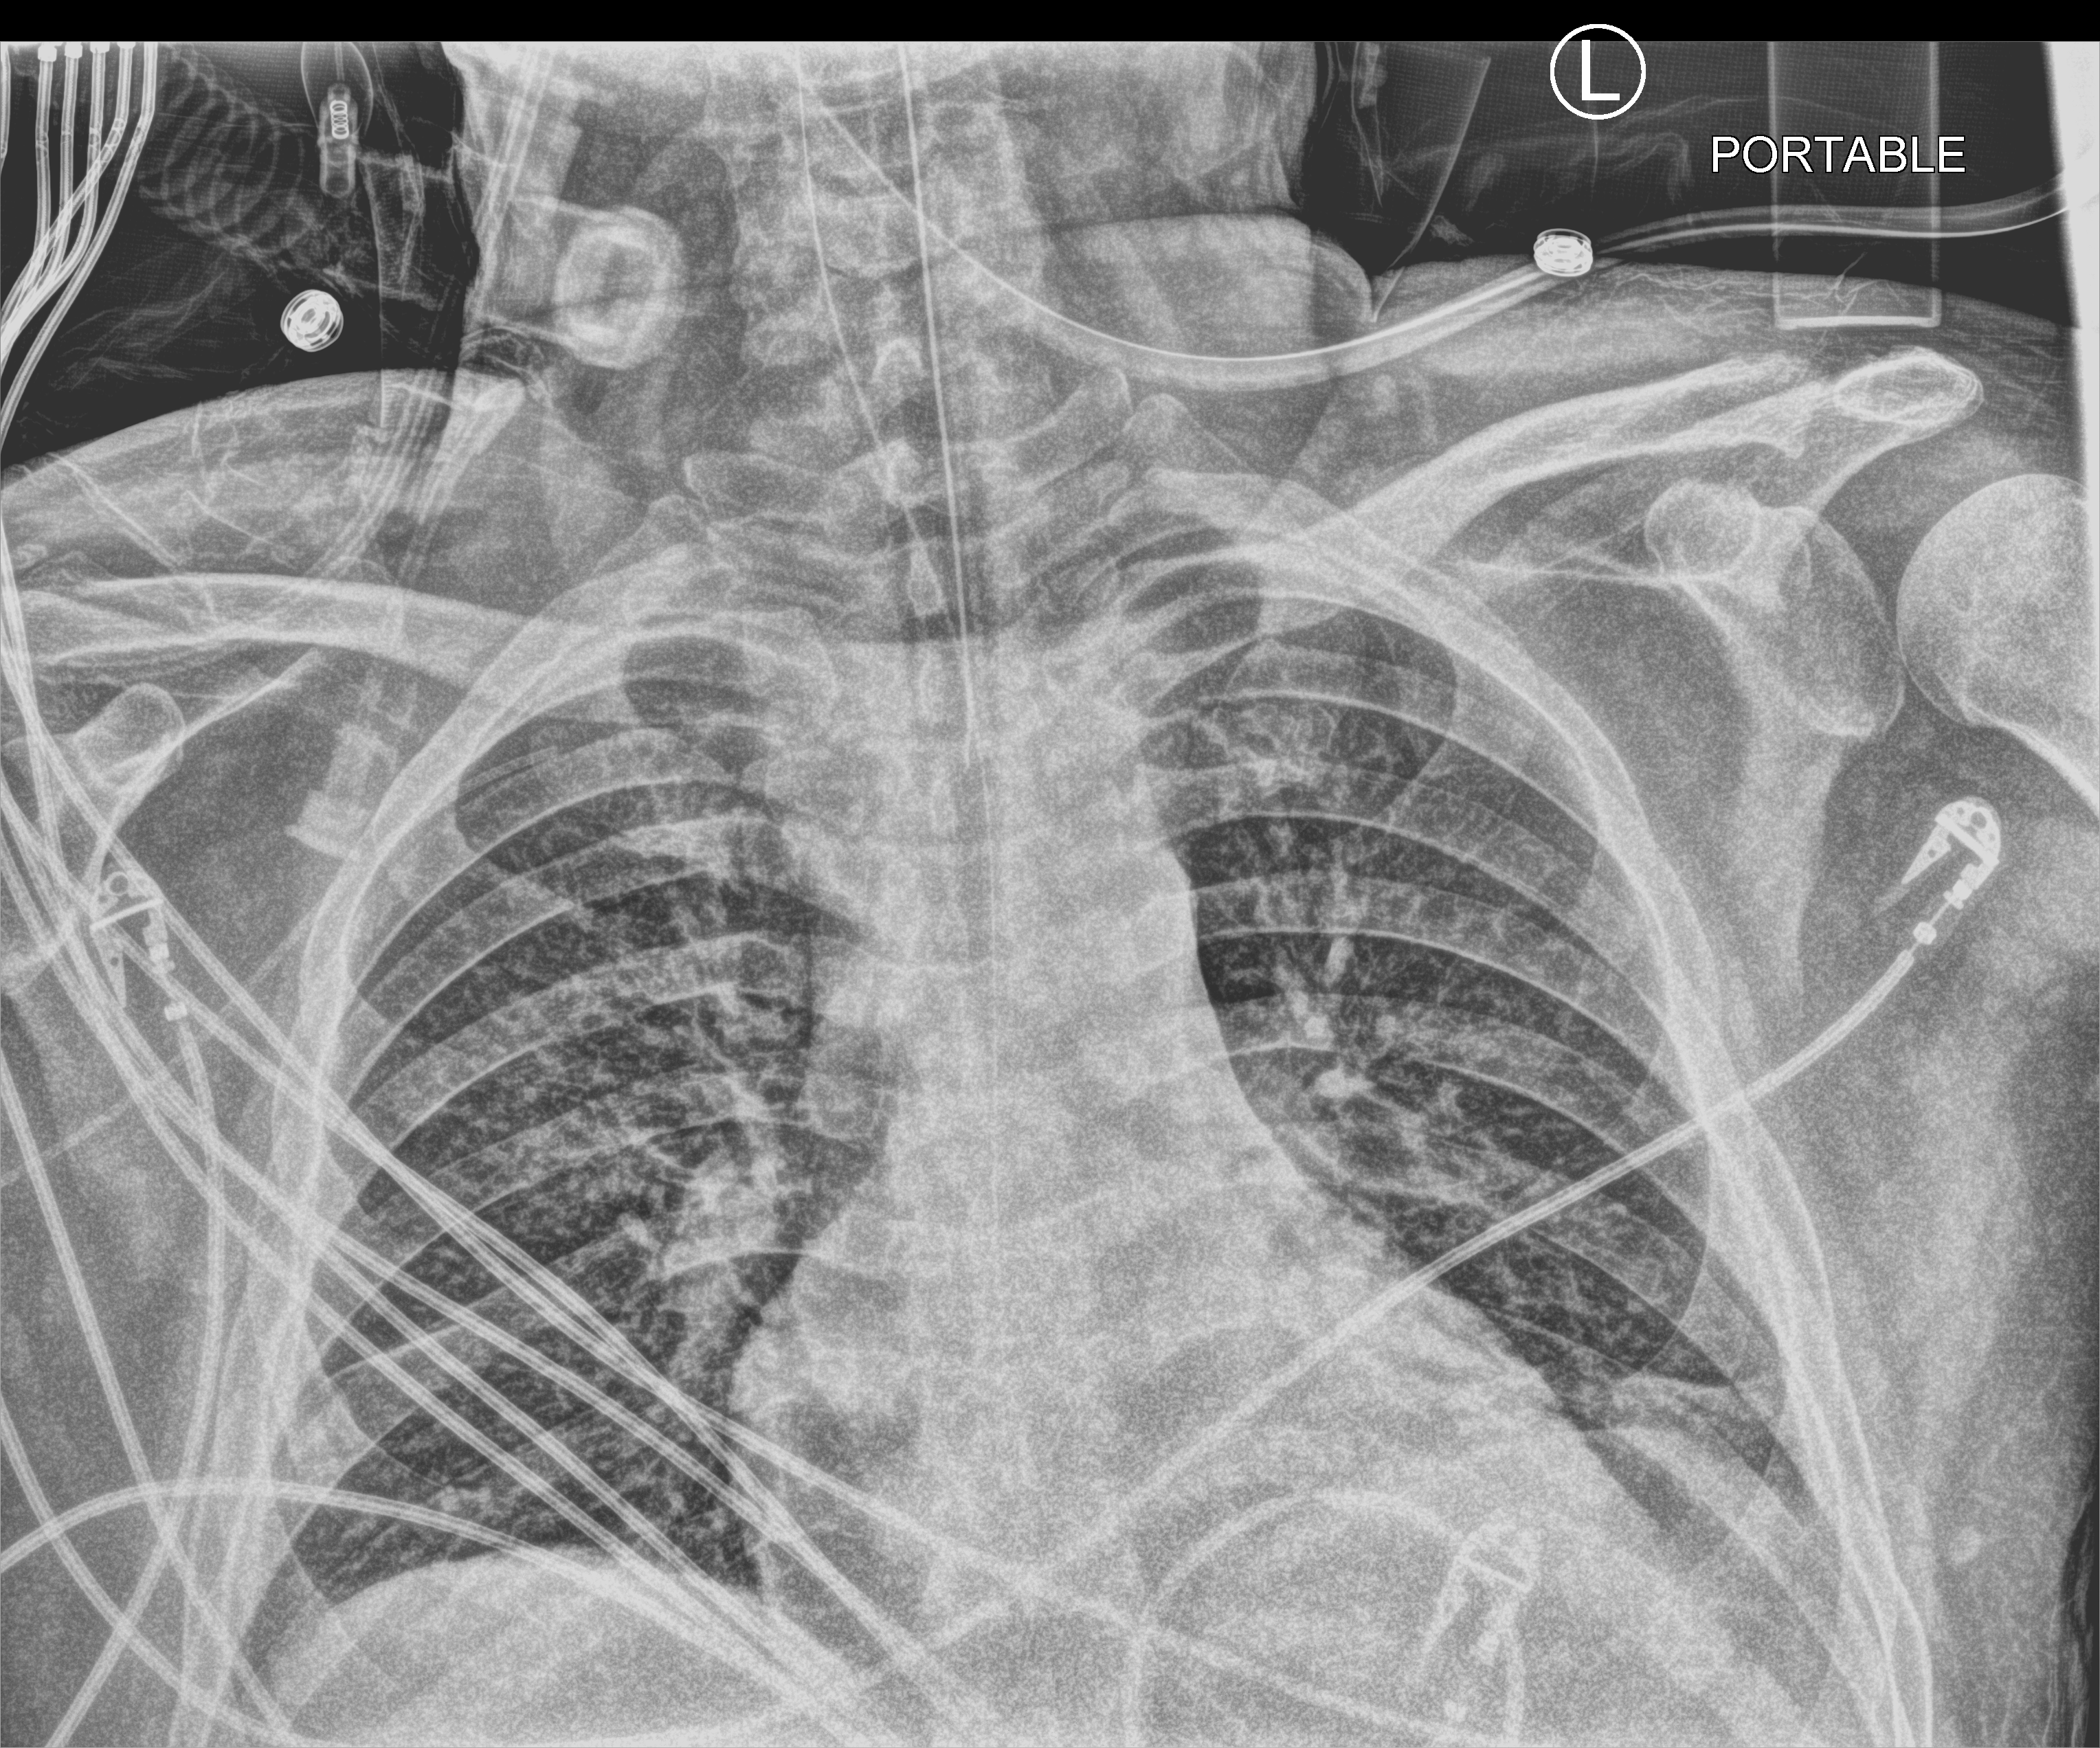
Chest X-ray (portable); anteroposterior (AP) projection. Patient hospitalised with COVID-19; male, aged 18–59 years.
Hospital-stay facts (about this admission, not read from this image; timing relative to this image not recorded): admitted to intensive care during this hospital stay: yes; mechanically ventilated during this hospital stay: yes.